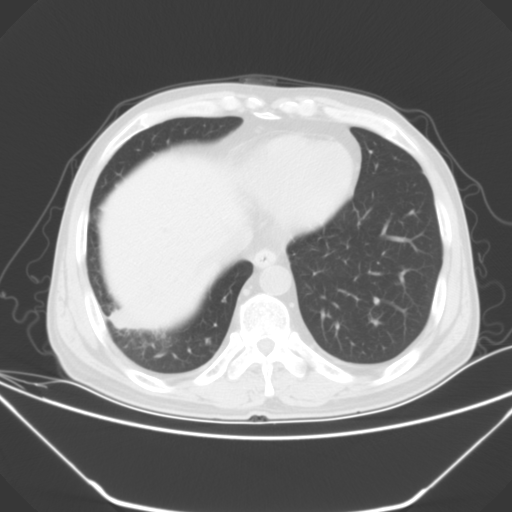
Chest CT, one axial slice. Position 12 of 52 along the scan axis. 120 kVp. Lung window (W 1500 / L -600 HU). 5 mm slice thickness. 512 × 512 image matrix, field of view 379 × 379 mm. Male patient, age 54 years. Case-level facts recorded for this patient, not image findings: clinical TNM (as recorded): T2 N1 M0; histopathological grade: G3.
Structures marked on this image (rectangle marked by the reading radiologist):
- lung tumour (recorded histology: adenocarcinoma): bounding box (x1, y1, x2, y2) in pixels: (109, 303, 135, 331)